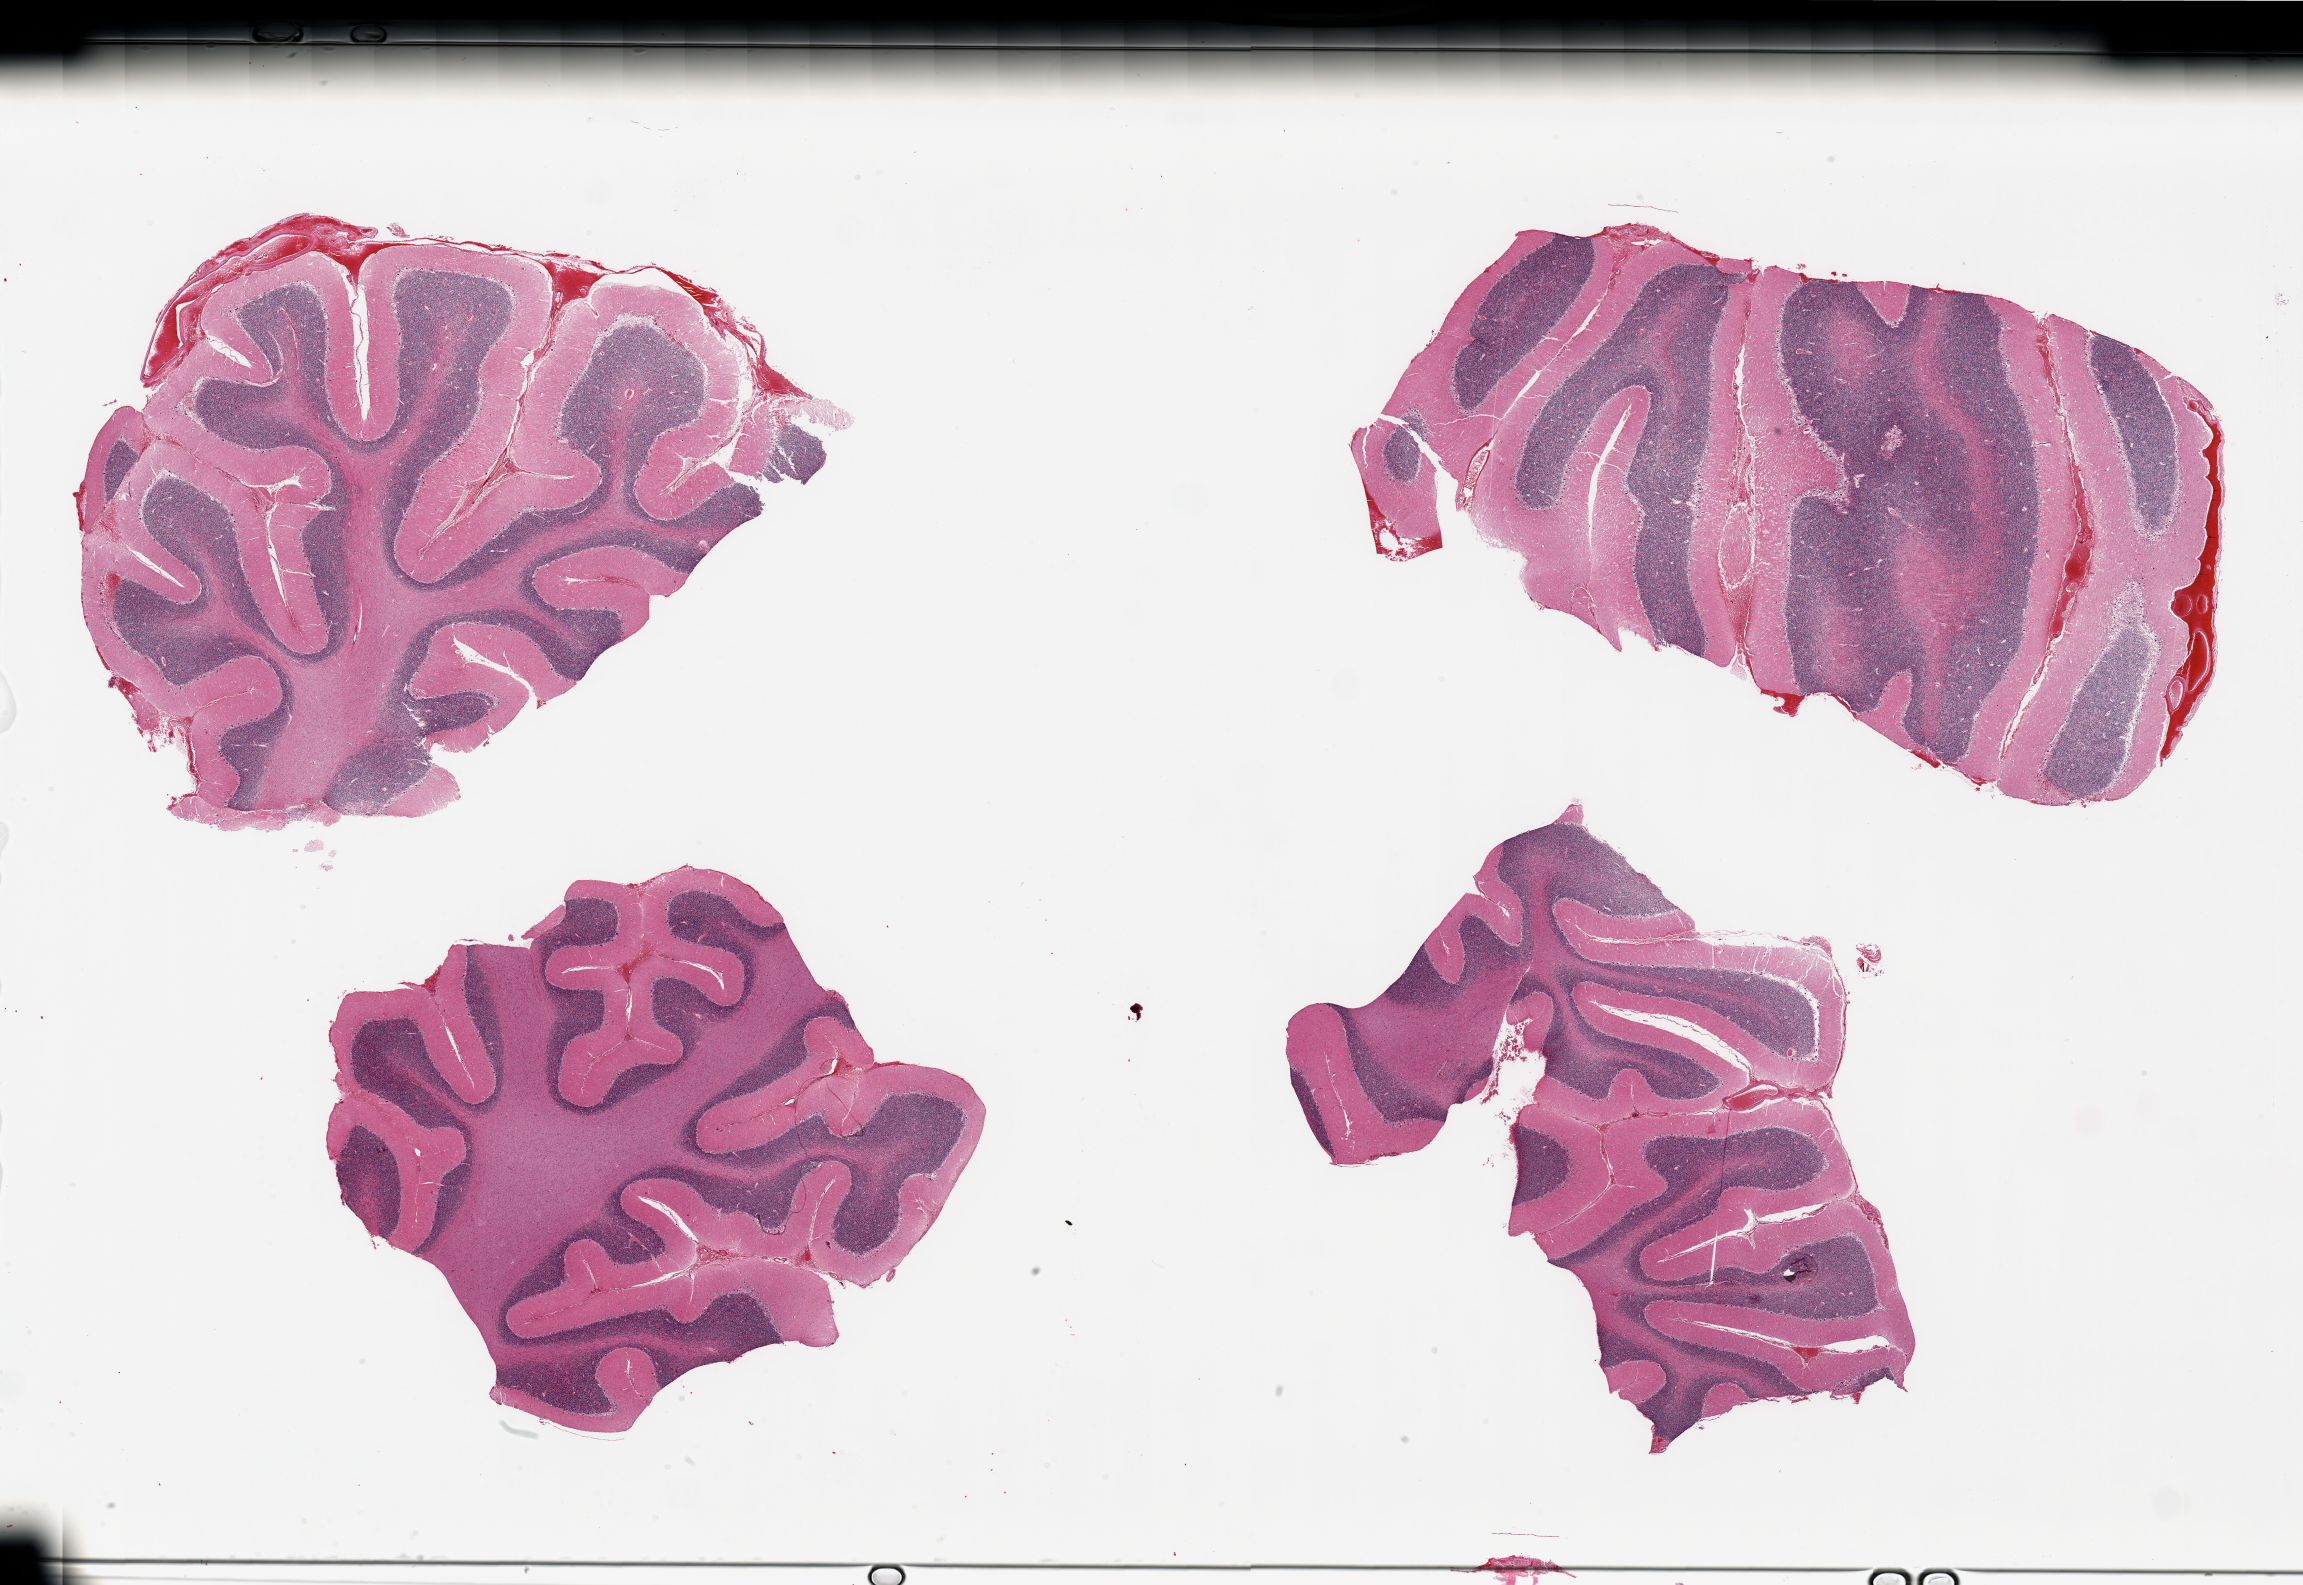
H&E whole-slide image, whole scanned area (about 36.4 x 25.1 mm, acquisition: 20x scan) shown as a low-resolution overview, PAXgene-fixed, paraffin-embedded tissue, section of cerebellum (target tissue), tissue donor sample. Donor sex: male.
Reviewer comment on this tissue sample: 4 pieces, no abnormalities.